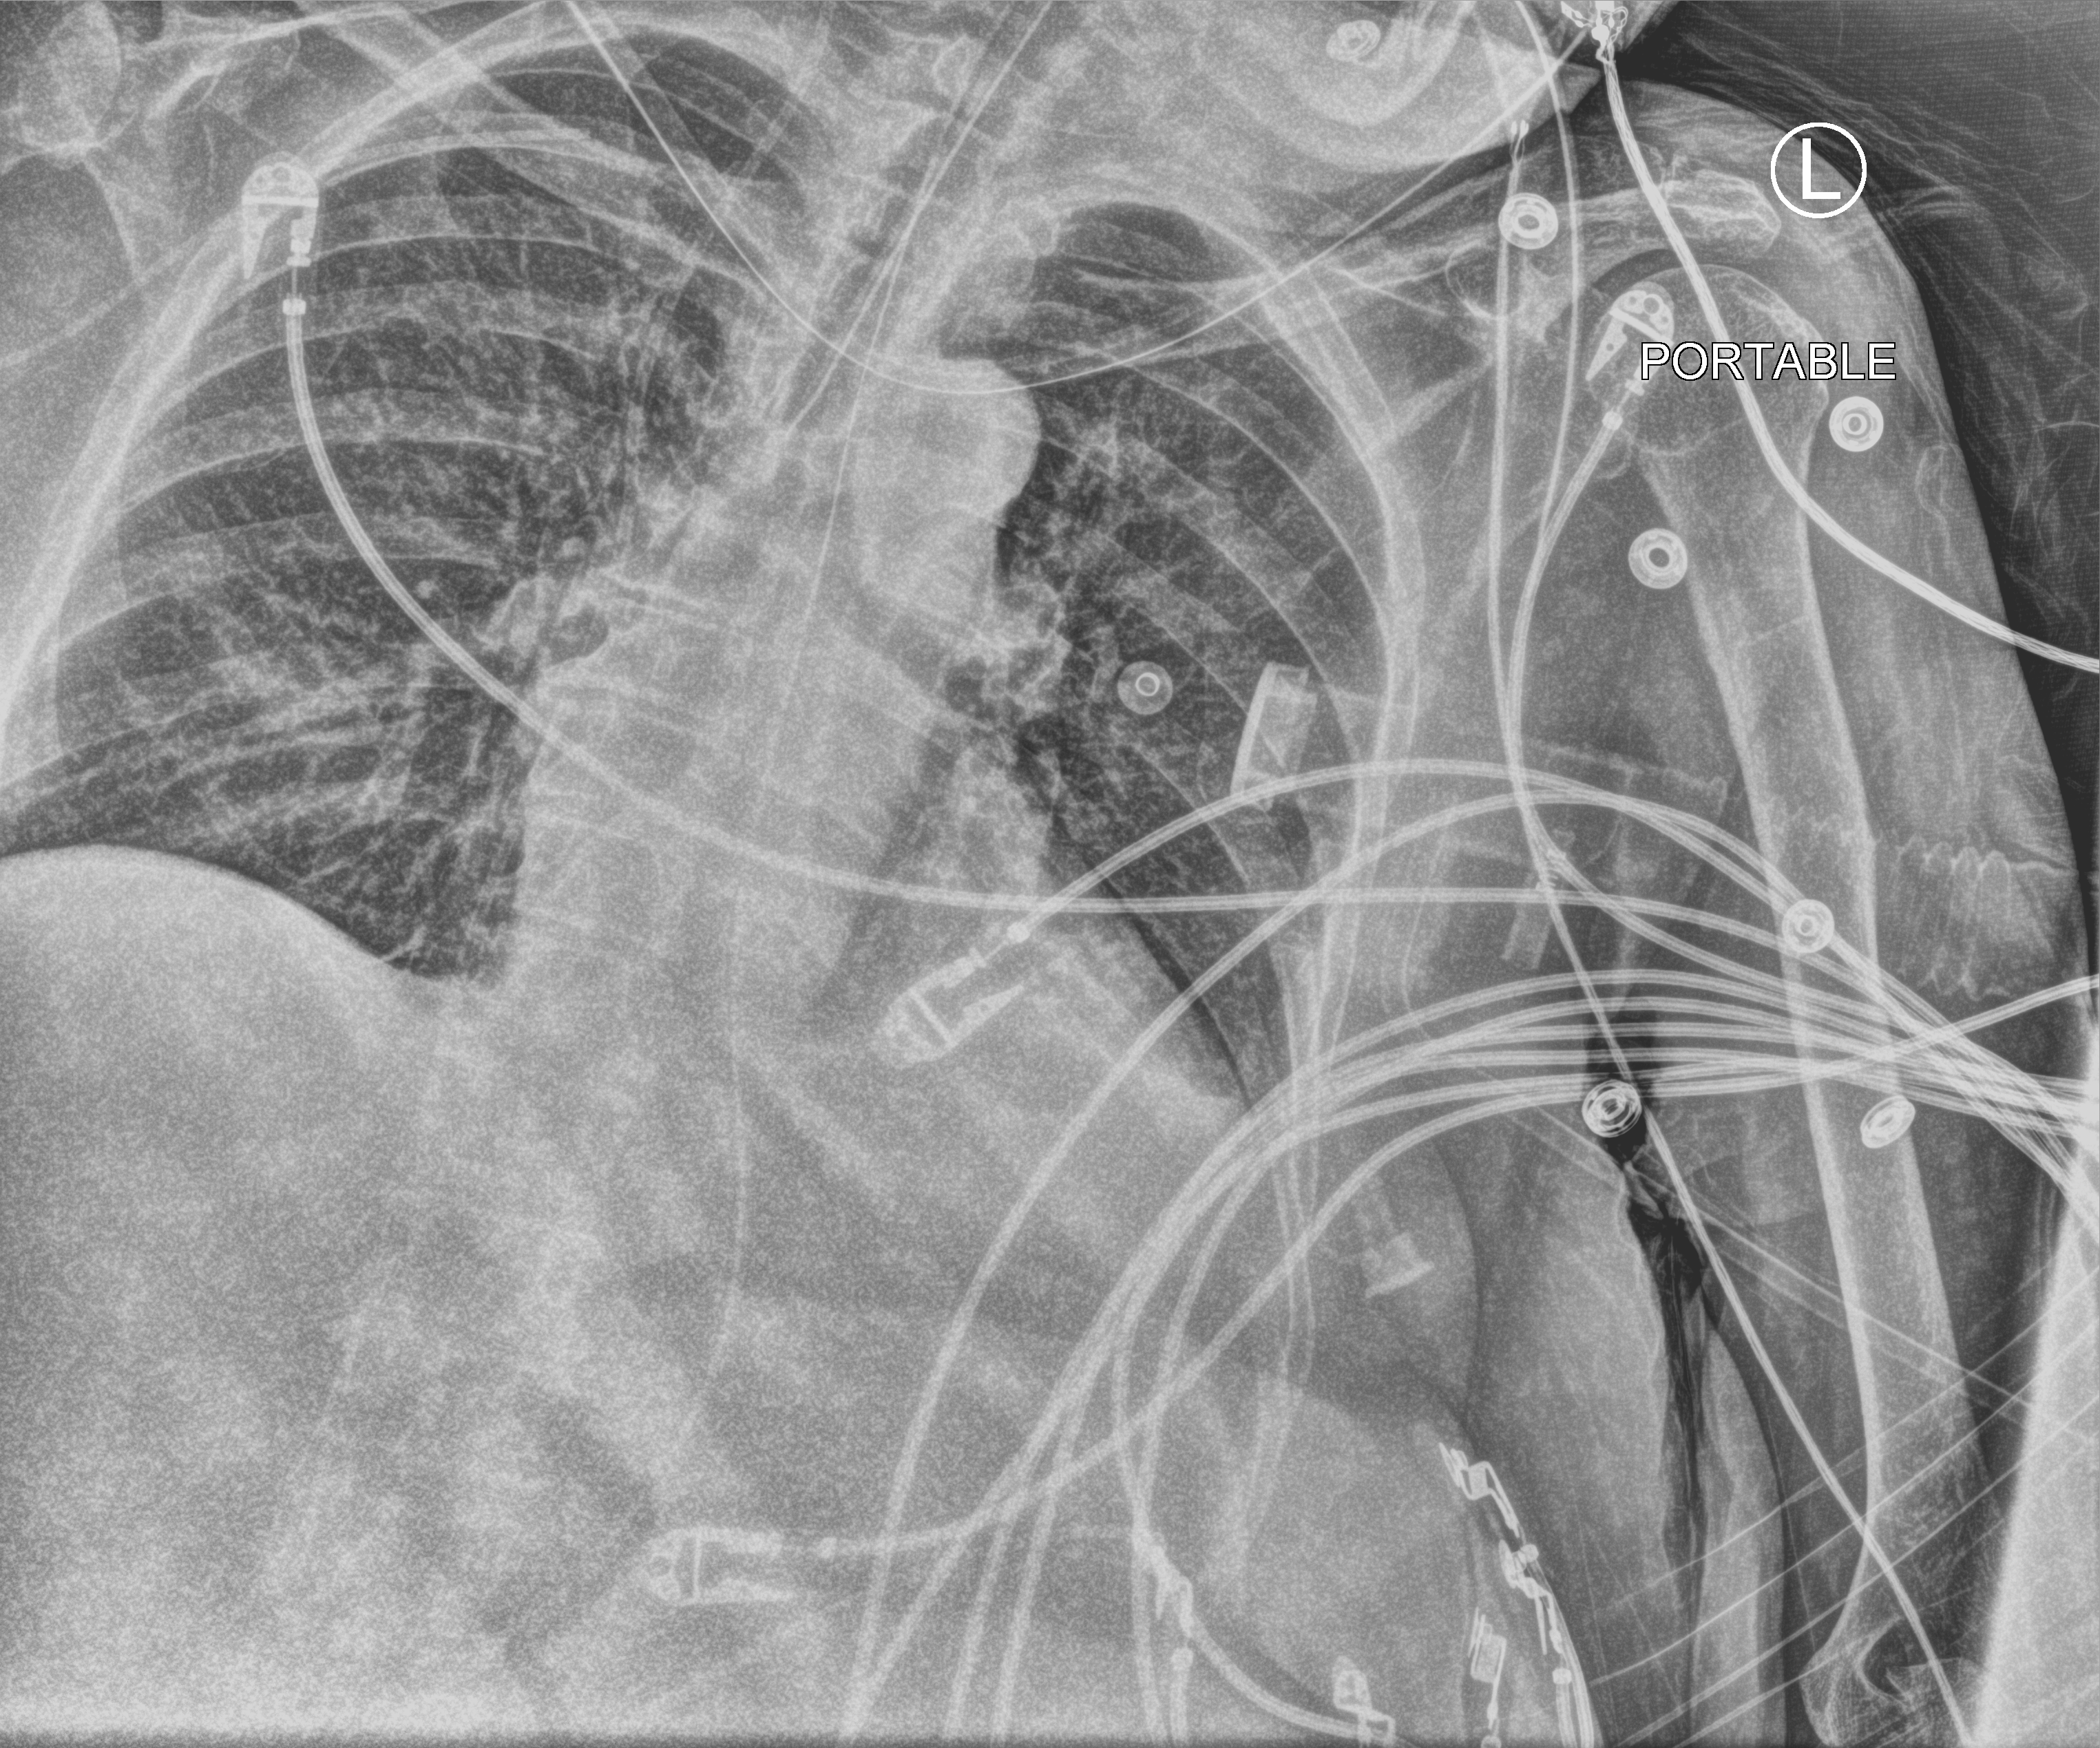
Portable chest radiograph. Patient hospitalised with COVID-19; female, aged 75–90 years.
Admission-level facts for this patient (not findings on this image; timing relative to this image not recorded): mechanically ventilated during this hospital stay: yes.